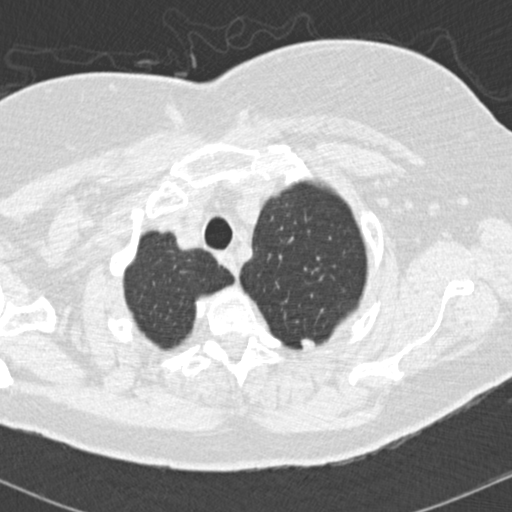
Low-dose screening chest CT, one axial slice; position 145 of 174 along the scan axis; reconstruction kernel B30f; 140 kVp; lung window (W 1500 / L -600 HU); 512 × 512 image matrix, field of view 310 × 310 mm.
Annotated regions visible in this slice (outlined manually by an expert reader):
- lesion 1 (tumor, upper lobe of left lung): bounding box (x1, y1, x2, y2) in pixels: (300, 334, 317, 351)